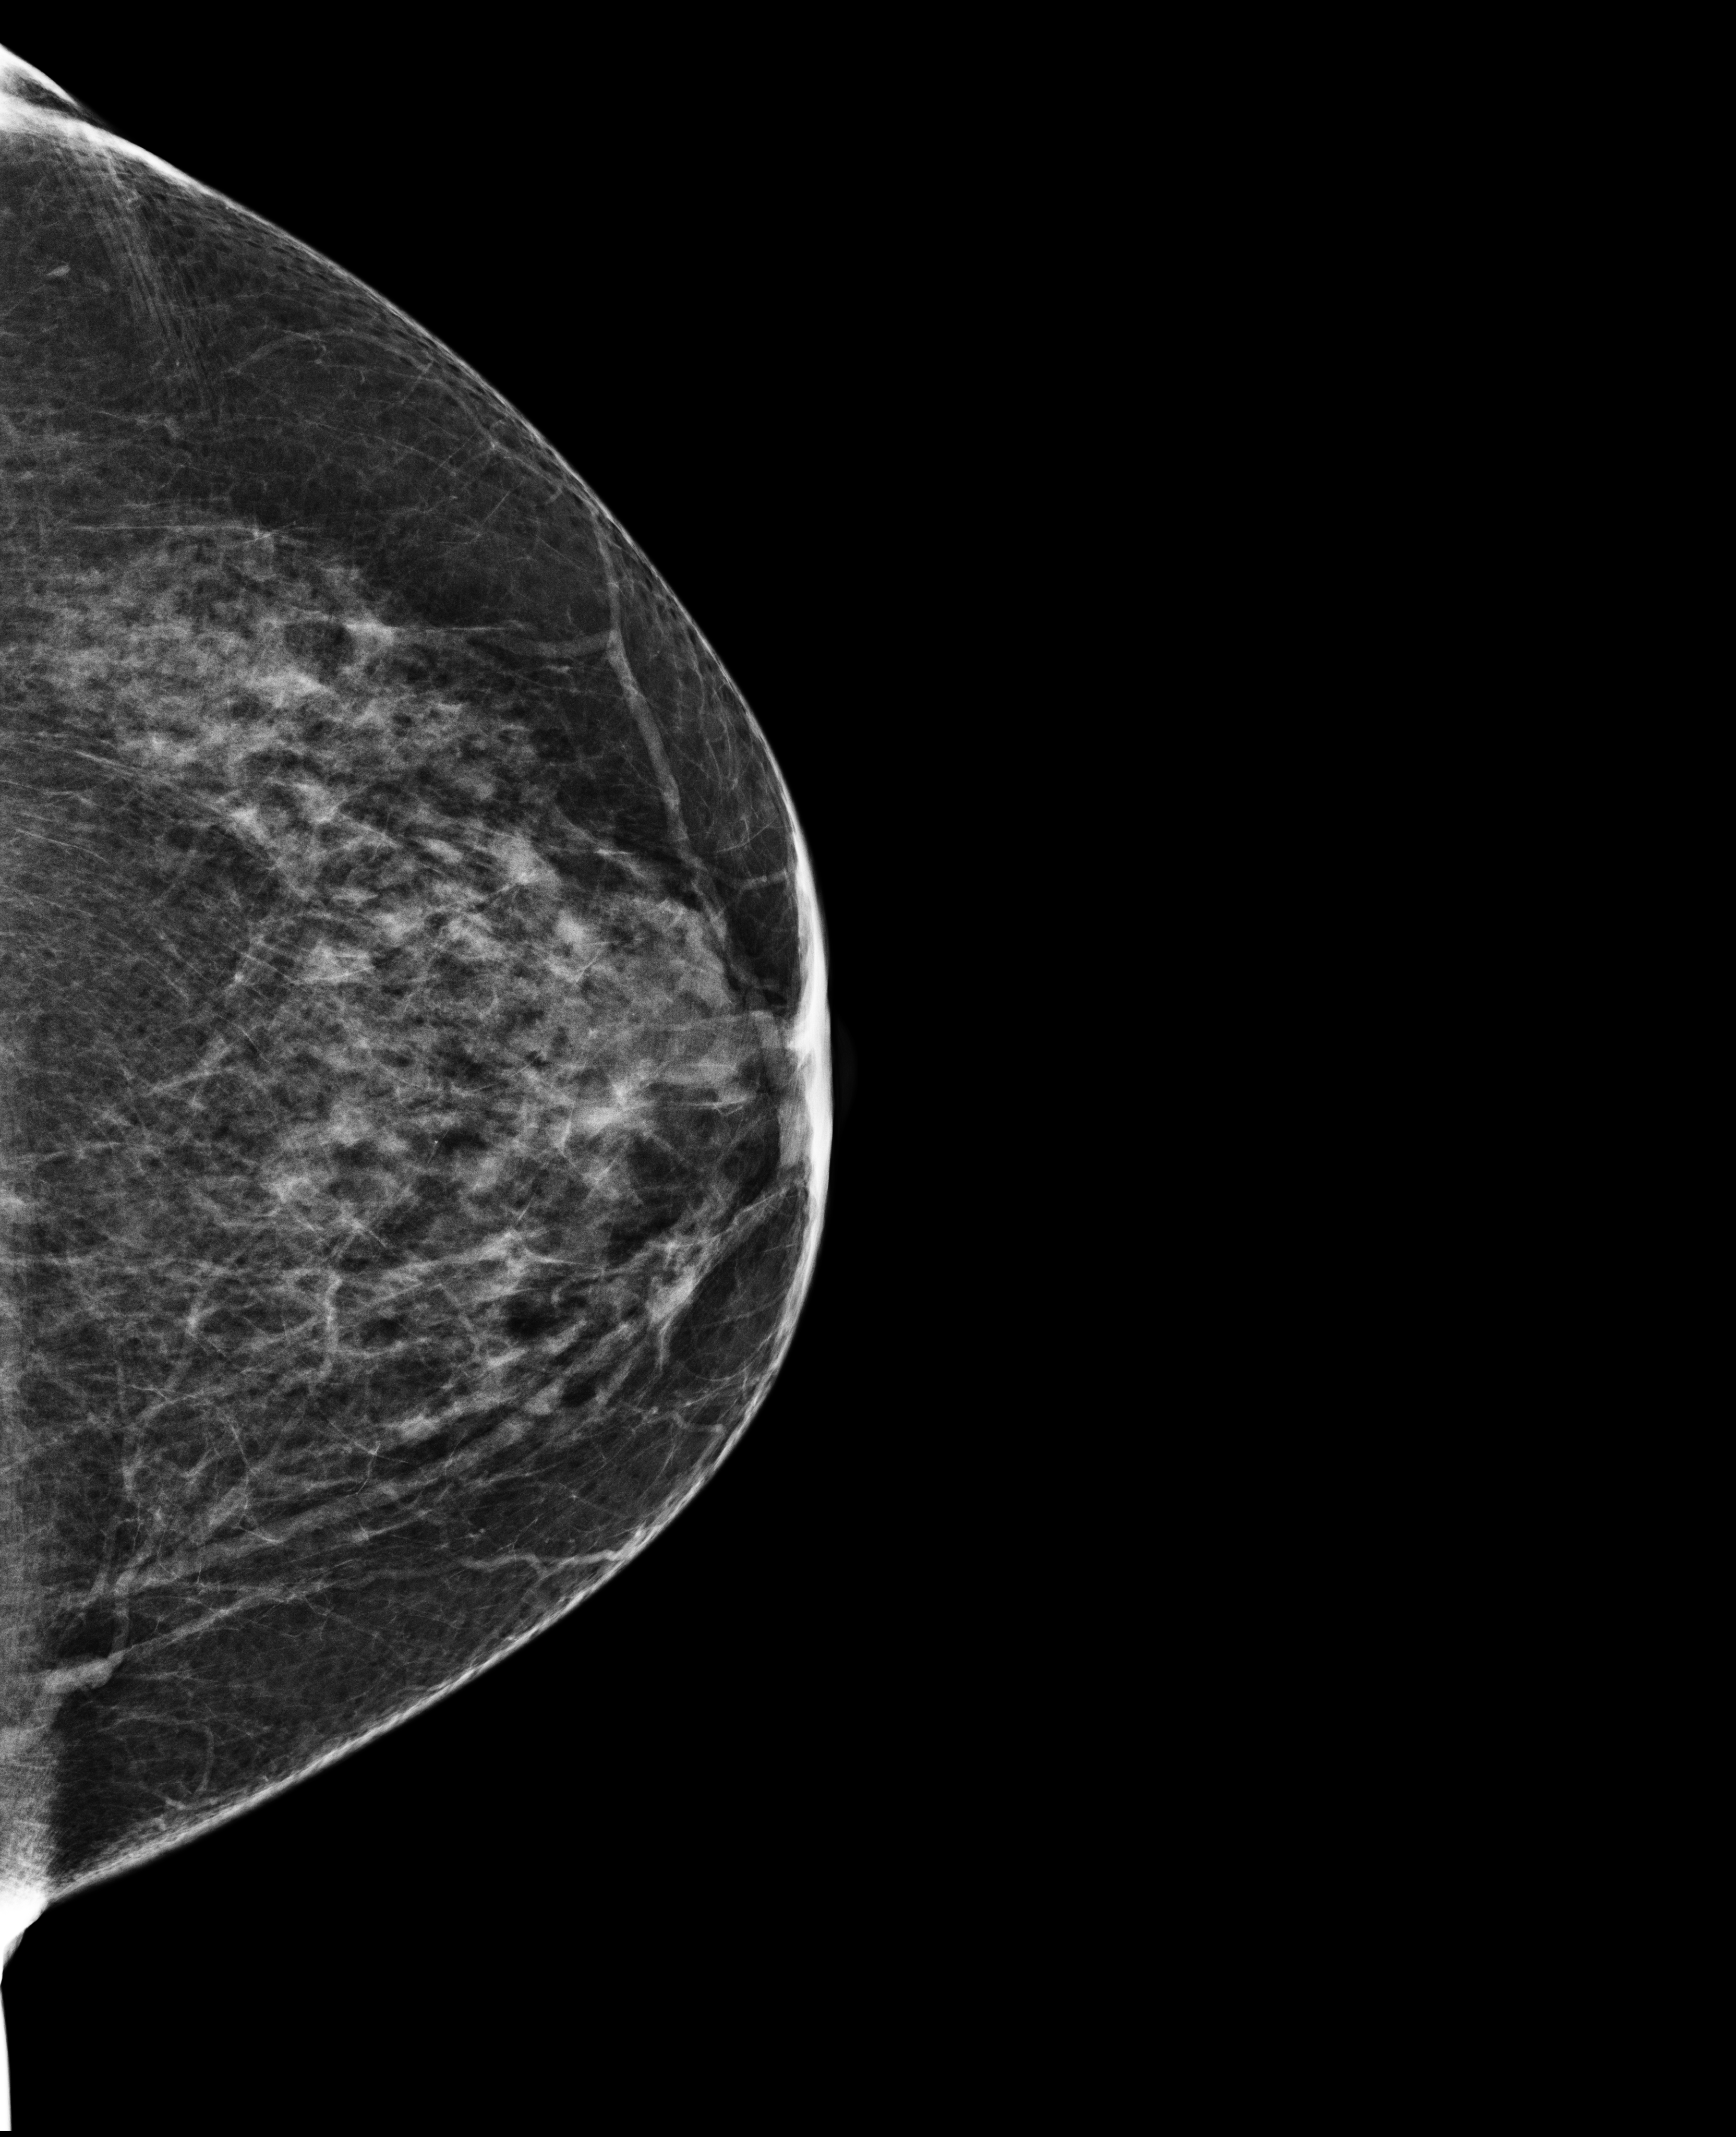
Screening examination, system: Selenia Dimensions. Patient: female, 72 years.
Image type: full-field digital mammogram. Breast: left. Projection: craniocaudal (CC) view.